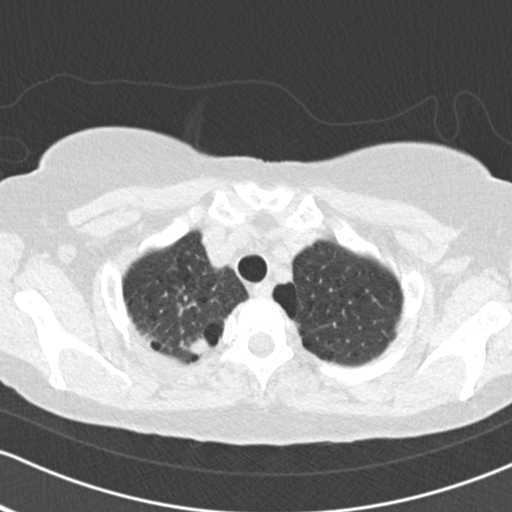
Low-dose screening chest CT, axial slice; second screening round (one year after baseline); lung window (W 1500 / L -600 HU); slice 17 of 161 in the series; 512 × 512 image matrix. Female, age 64 years at enrolment.
- Lesion marked by an expert reader, bounding box <173,325,220,368> (left, top, right, bottom; pixels).
- Screening reader's record for this exam (one nodule recorded; not confirmed to be the boxed lesion): non-calcified nodule or mass ≥4 mm, right upper lobe, 16 × 15 mm, spiculated (stellate) margins, soft tissue attenuation, pre-existing on the prior screen: no.
- Official screen result: positive, other.
- Later outcome: lung cancer diagnosed 45 days after this screen — adenocarcinoma, NOS, right upper lobe, poorly differentiated (G3), stage IB (AJCC 6th edition), 15 mm at pathology.